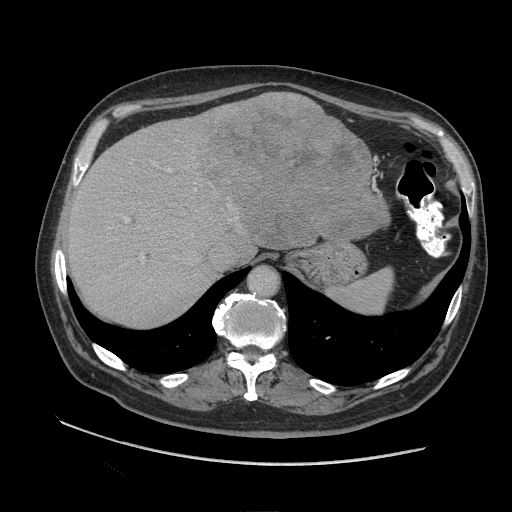
Contrast-enhanced abdominal CT (liver protocol), one axial slice; position 73 of 109 along the scan axis; reconstruction kernel STANDARD; soft-tissue window (W 400 / L 40 HU); 2.5 mm slice thickness; 512 × 512 image matrix, field of view 420 × 420 mm. From the clinical record (not read from this slice): diagnosis: hepatocellular carcinoma (patient treated with transarterial chemoembolisation; whether this scan precedes or follows treatment is not stated here); TNM stage (as recorded): Stage-I; Child-Pugh class: A.
Annotated regions visible in this slice (semi-automatic segmentation, software-assisted and operator-edited):
- abdominal aorta: bounding box <250,267,277,297> (left, top, right, bottom; pixels)
- liver parenchyma outside the tumour (the mass and vessels are separate outlines, so this box may not span the whole liver): <66,92,390,326>
- mass: <196,92,390,248>
- liver vessels: <125,165,196,259>